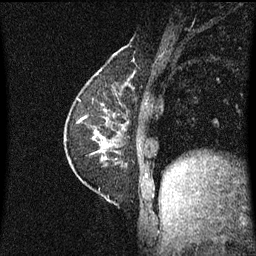
Breast MRI (dynamic contrast-enhanced), one sagittal slice; position 19 of 60 along the scan axis; dynamic contrast-enhanced series, image 2 of 3 at this slice position (ordered by acquisition); 1.5 T; TE 4.2 ms, TR 8.4 ms; 2 mm slice thickness; 256 × 256 image matrix, field of view 200 × 200 mm. Patient: female, 60 years.
Annotated regions visible in this slice (semi-automatically segmented with operator editing):
- analysis volume of interest (the breast-tissue region the enhancement analysis was run in; not a lesion): bounding box [x1, y1, x2, y2] px = [69, 66, 133, 193]
- tumour enhancement mask (voxels above the 70 % enhancement threshold inside the analysis volume of interest): [96, 70, 129, 161]